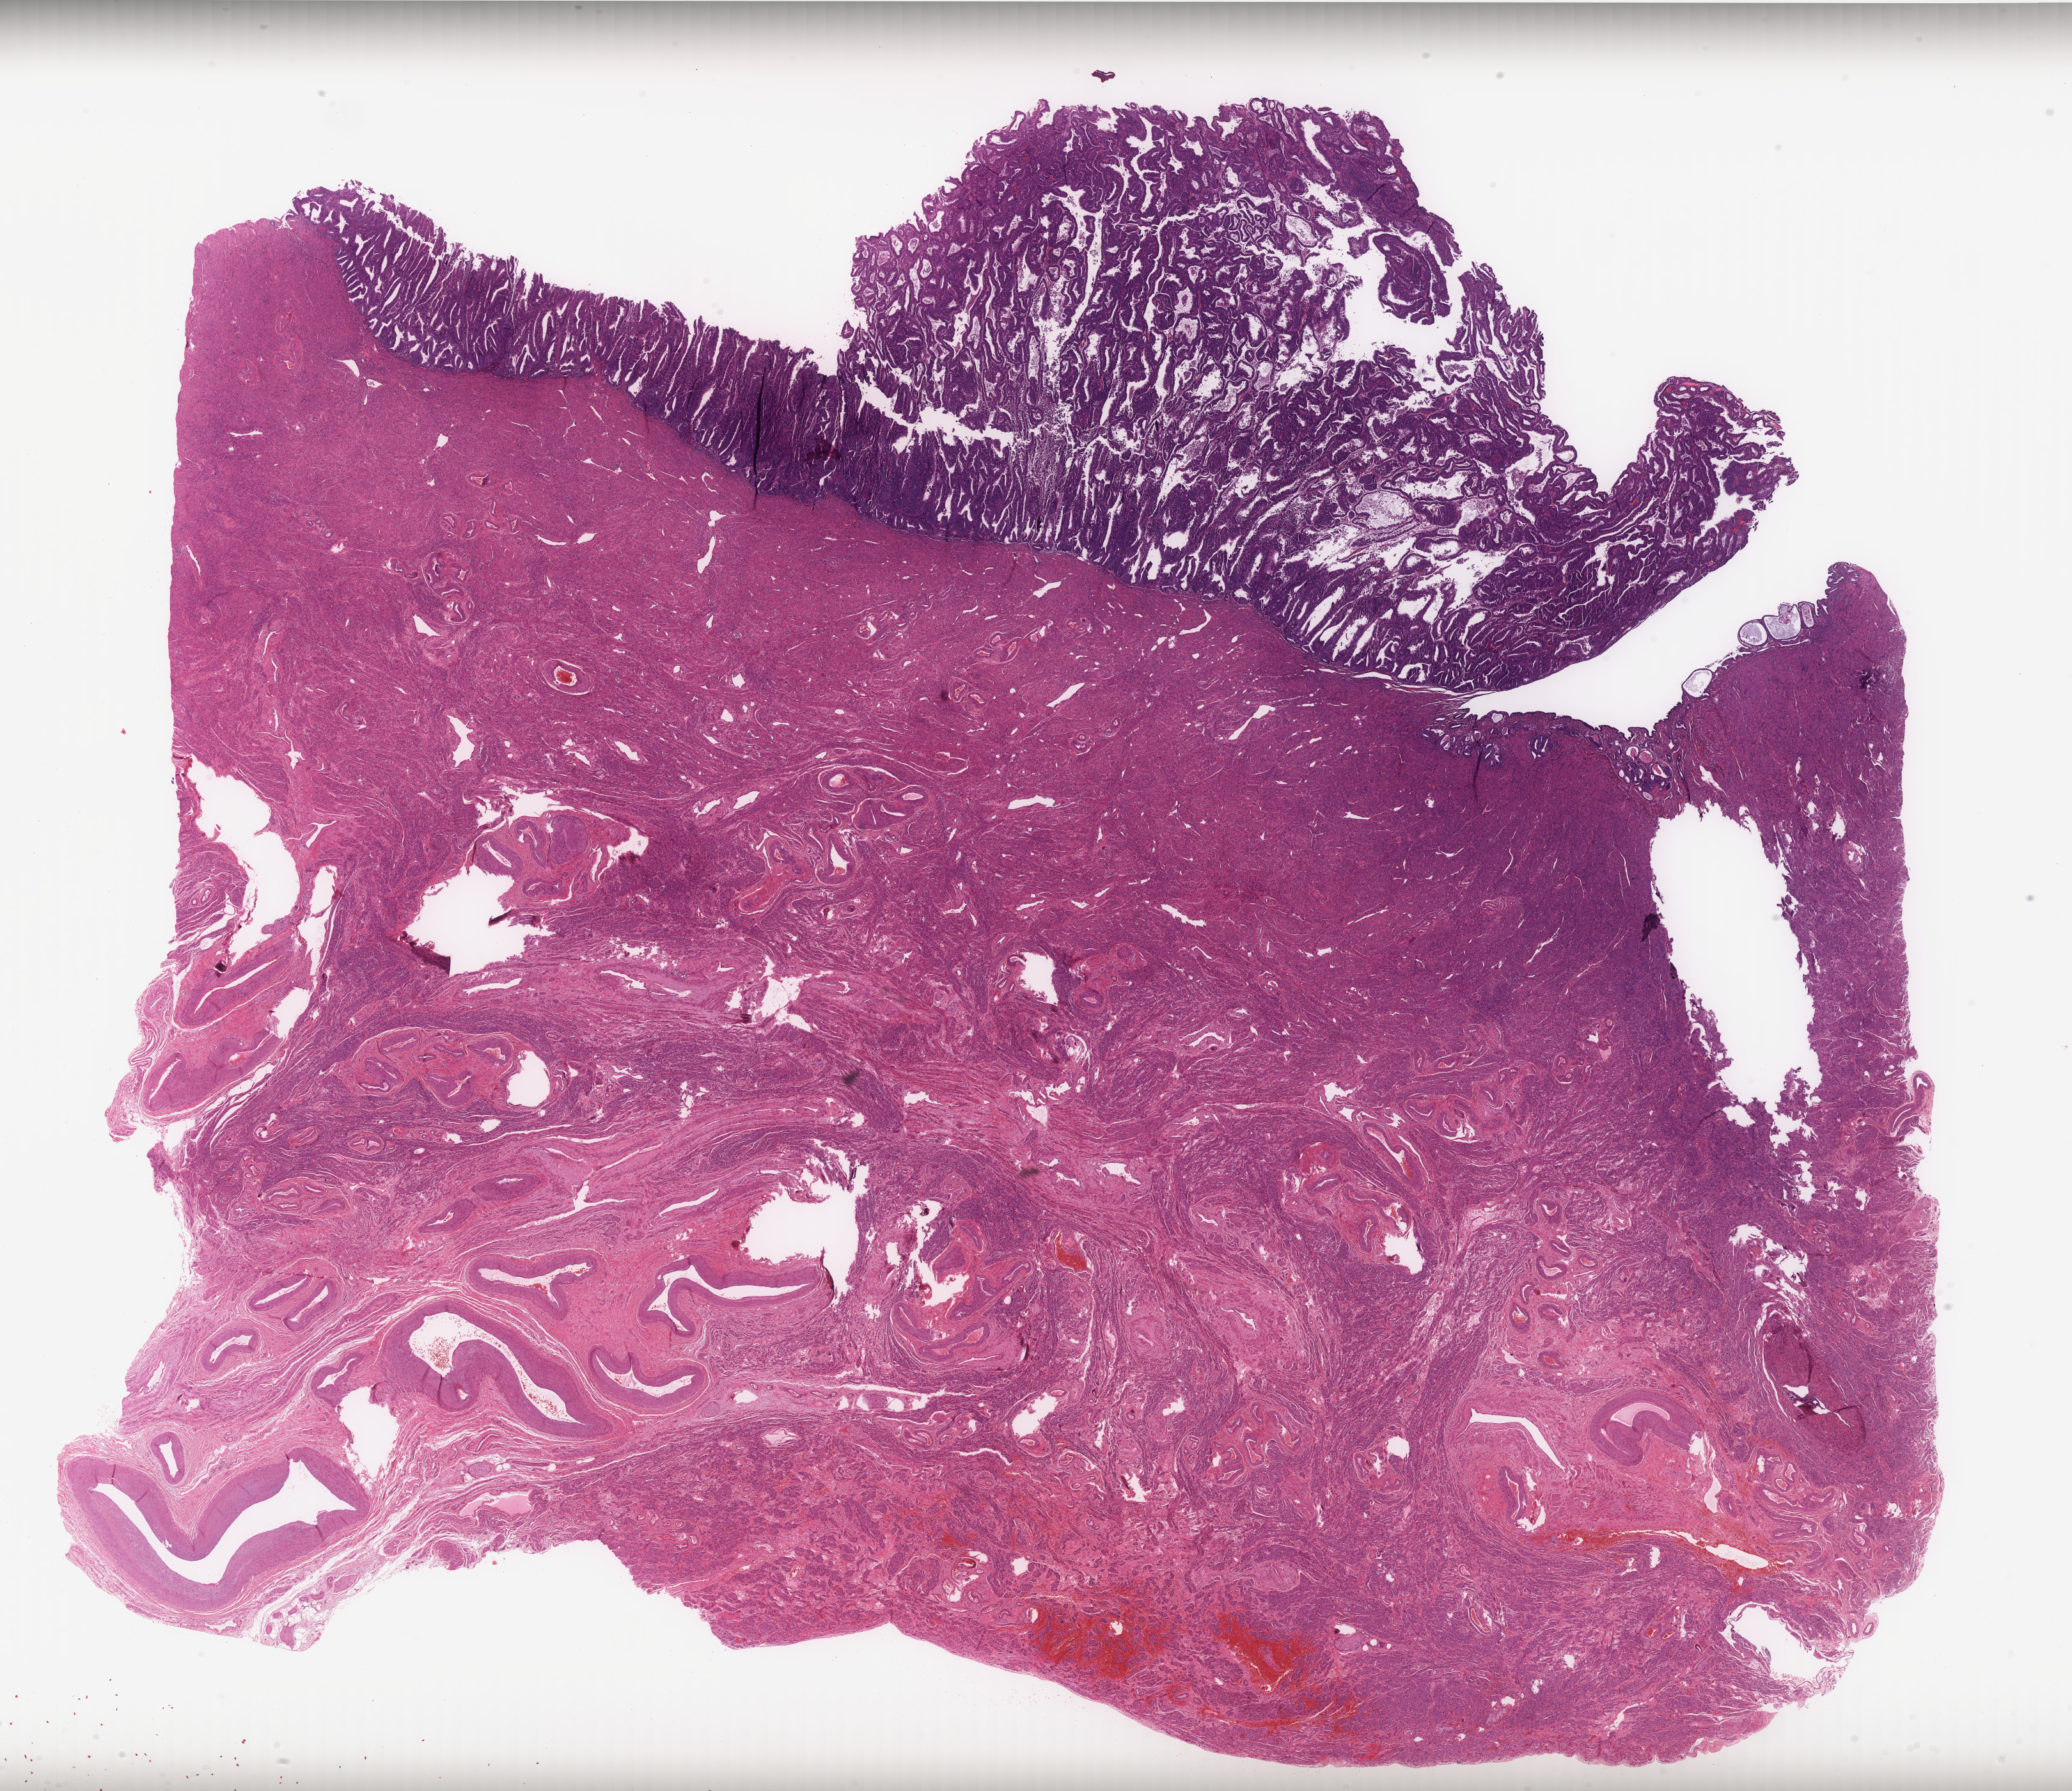
Digitized H&E tissue section (whole slide) — shown as a low-resolution overview of the whole scanned area (about 26.0 x 22.4 mm), FFPE section, primary tumour sample from the uterus. Female patient; age at initial diagnosis 75 years. Histologic grade: G2 (moderately differentiated).
• FIGO stage: IA
• histologic diagnosis: Endometrioid adenocarcinoma, NOS (endometrium)